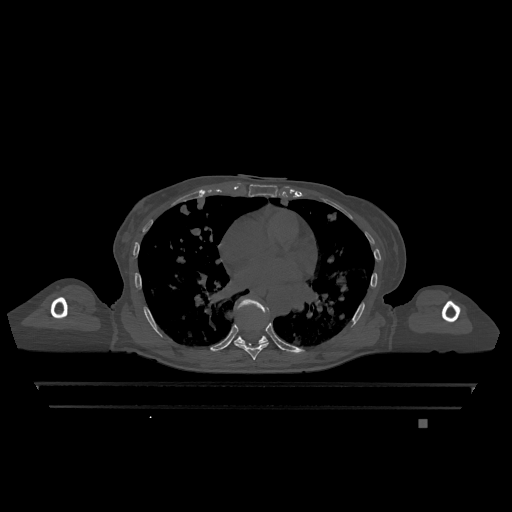
CT including the spine, one axial slice. Slice 720 of 1317 in the series (ordered by position). Bone window (W 1800 / L 400 HU). 0.5 mm slice thickness. 512 × 512 image matrix, field of view 500 × 500 mm. Patient: female, 74 years. From the clinical record (not read from this slice): primary cancer: lung; vertebrae with lytic lesions (as recorded): T1, T4, T5, T6, L4, L5.
Structures marked on this image (semi-automatically segmented with operator editing):
- T7 vertebra: box from (x=235, y=326) to (x=269, y=360) px
- T9 vertebra: (x=234, y=298)–(x=269, y=345)